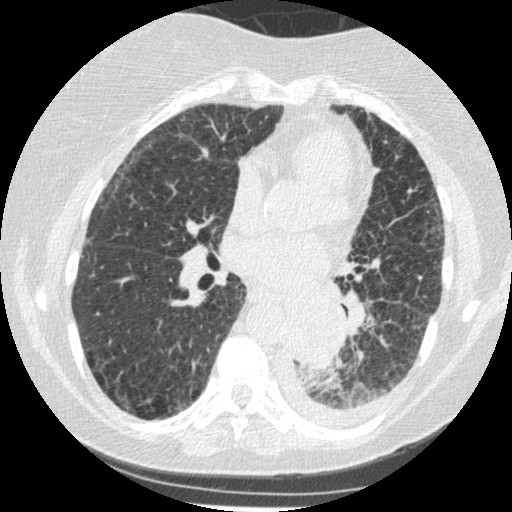
Axial slice from a low-dose chest CT screening exam, third annual screen, lung window (W 1500 / L -600 HU). Female, age 60 years at enrolment. Former smoker at enrolment.
• Expert-annotated lung lesion, box from (x=274, y=304) to (x=342, y=375) px.
• Reader record for this screening exam (exam-level; its link to the box is not recorded): non-calcified nodule or mass ≥4 mm, left lower lobe, 54 × 38 mm, smooth margins, soft tissue attenuation, pre-existing on the prior screen: yes; interval growth: yes.
• Official screen result: positive, other.